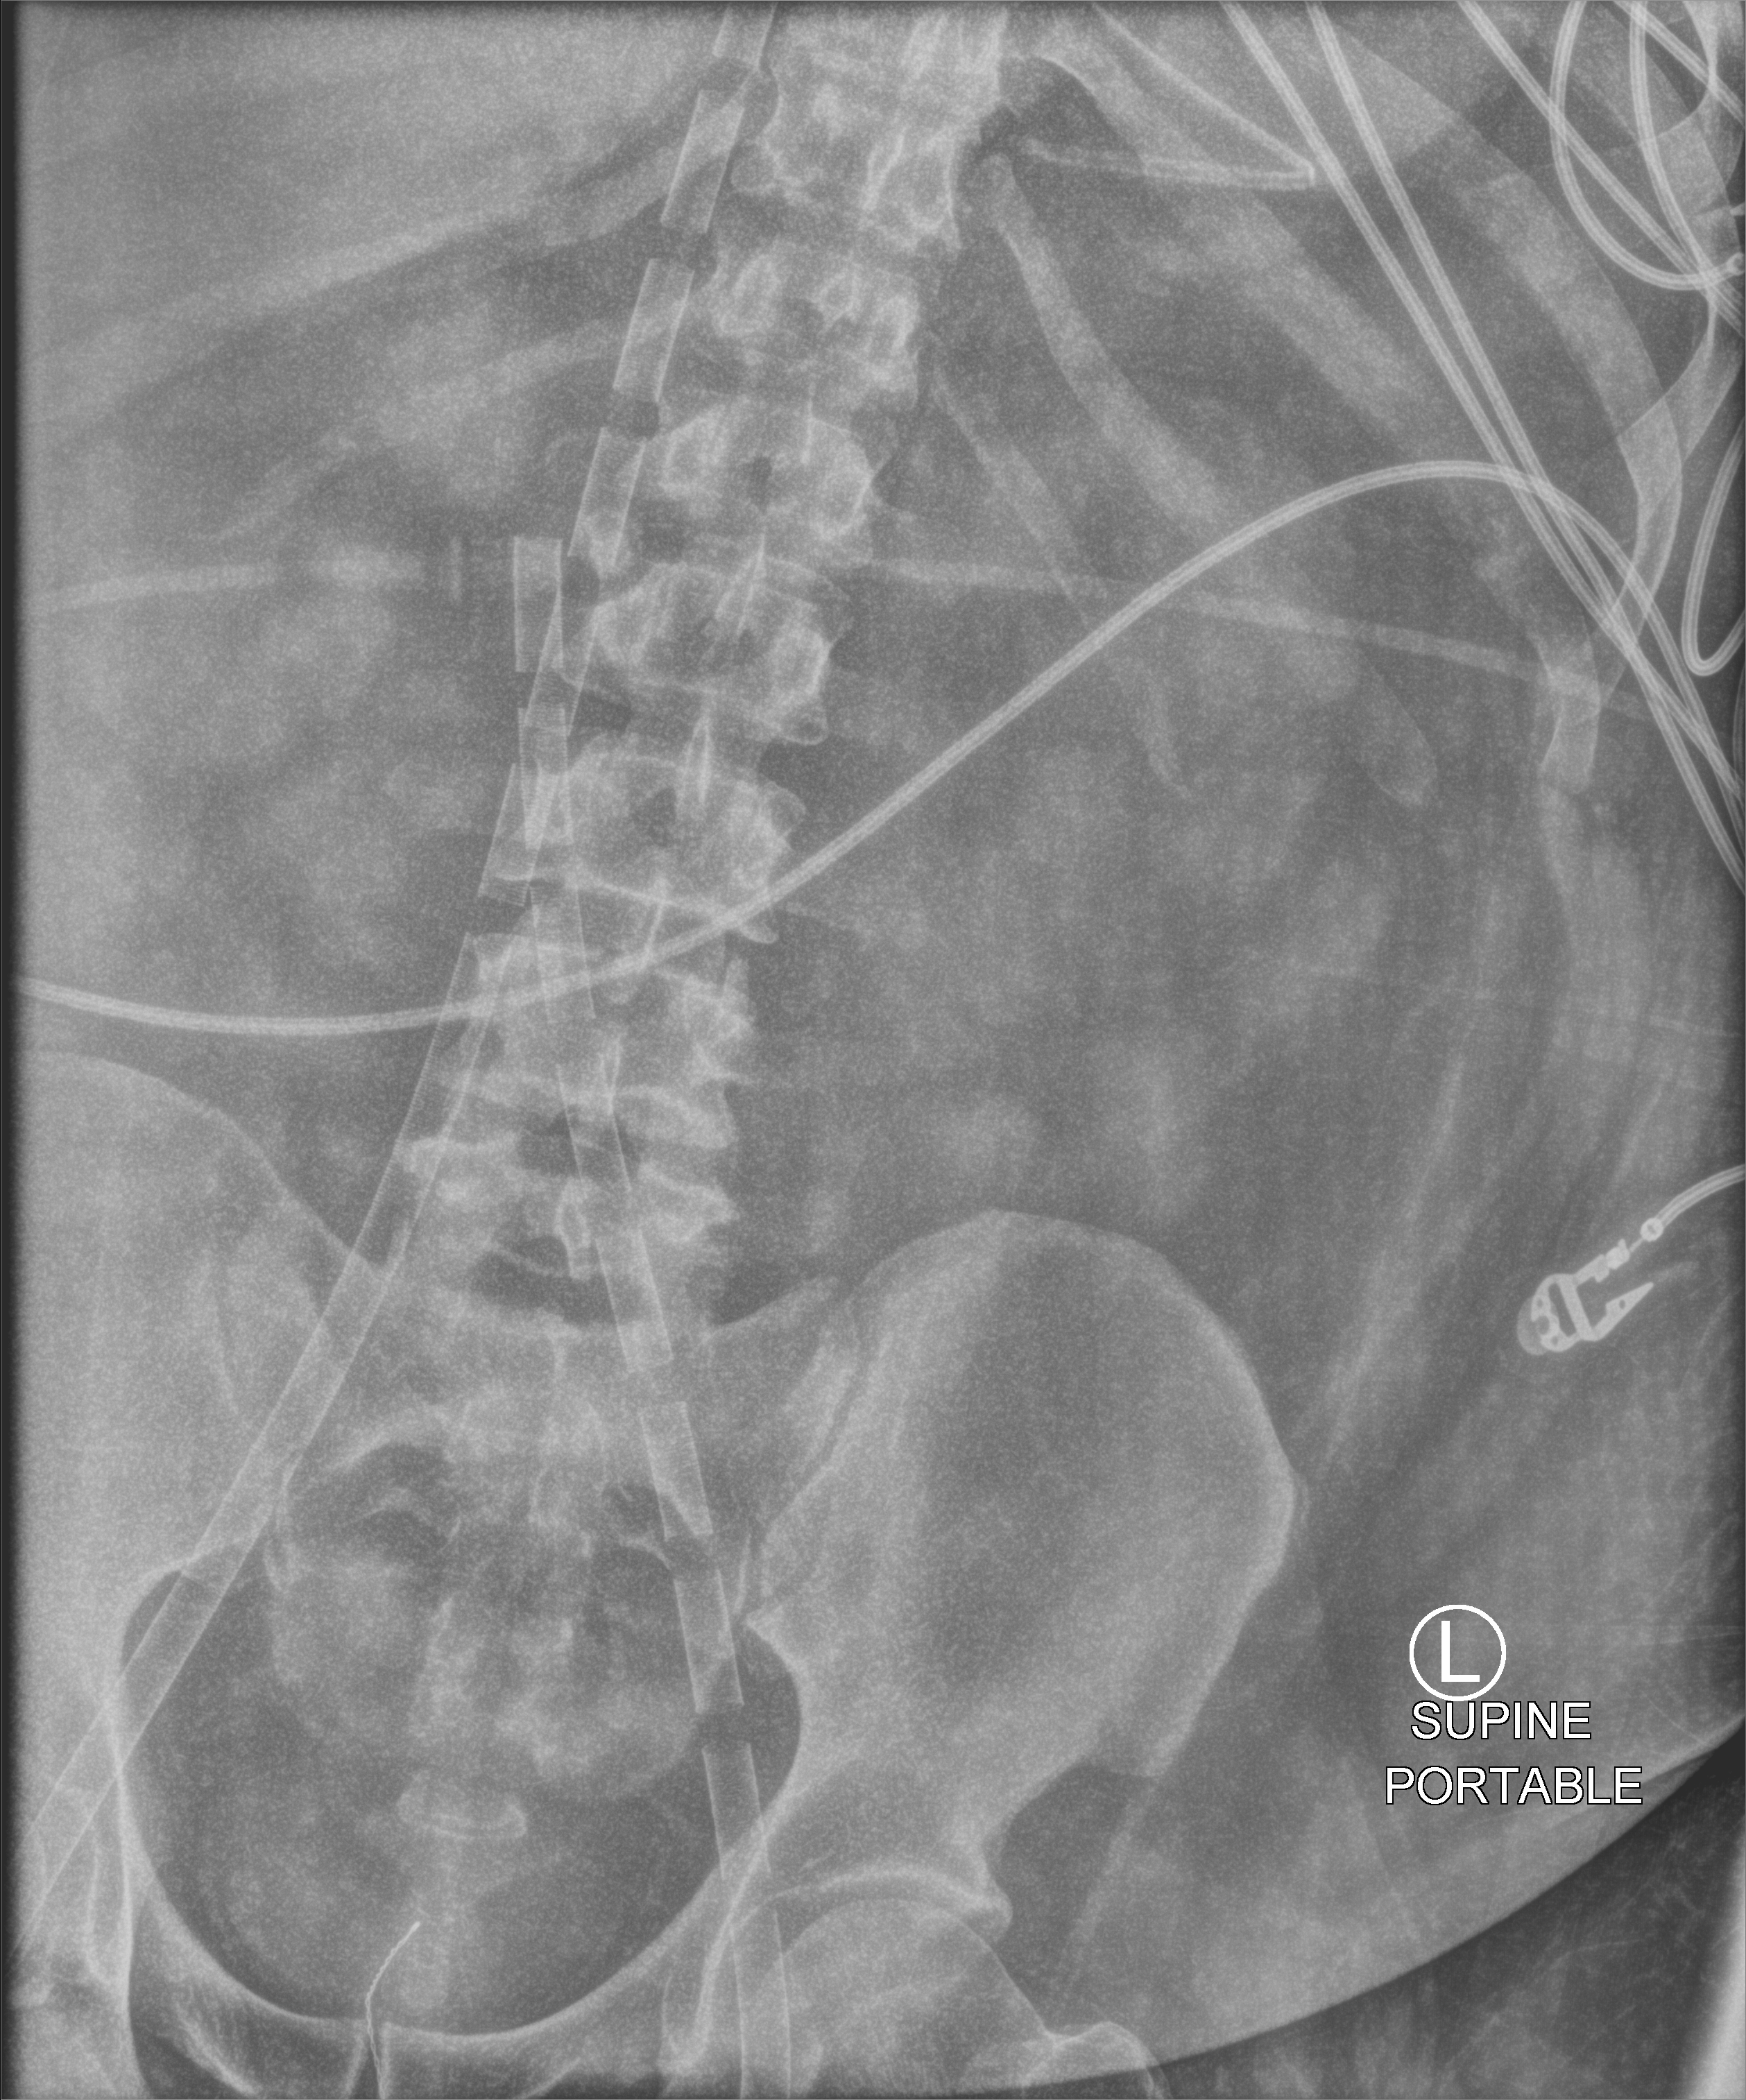
Portable abdomen radiograph; anteroposterior (AP) projection. Adult patient hospitalised with COVID-19, age 18–59 years.
From the hospital-stay record, not from the radiograph (when in the stay this image was taken is not recorded): mechanically ventilated during this hospital stay: yes.